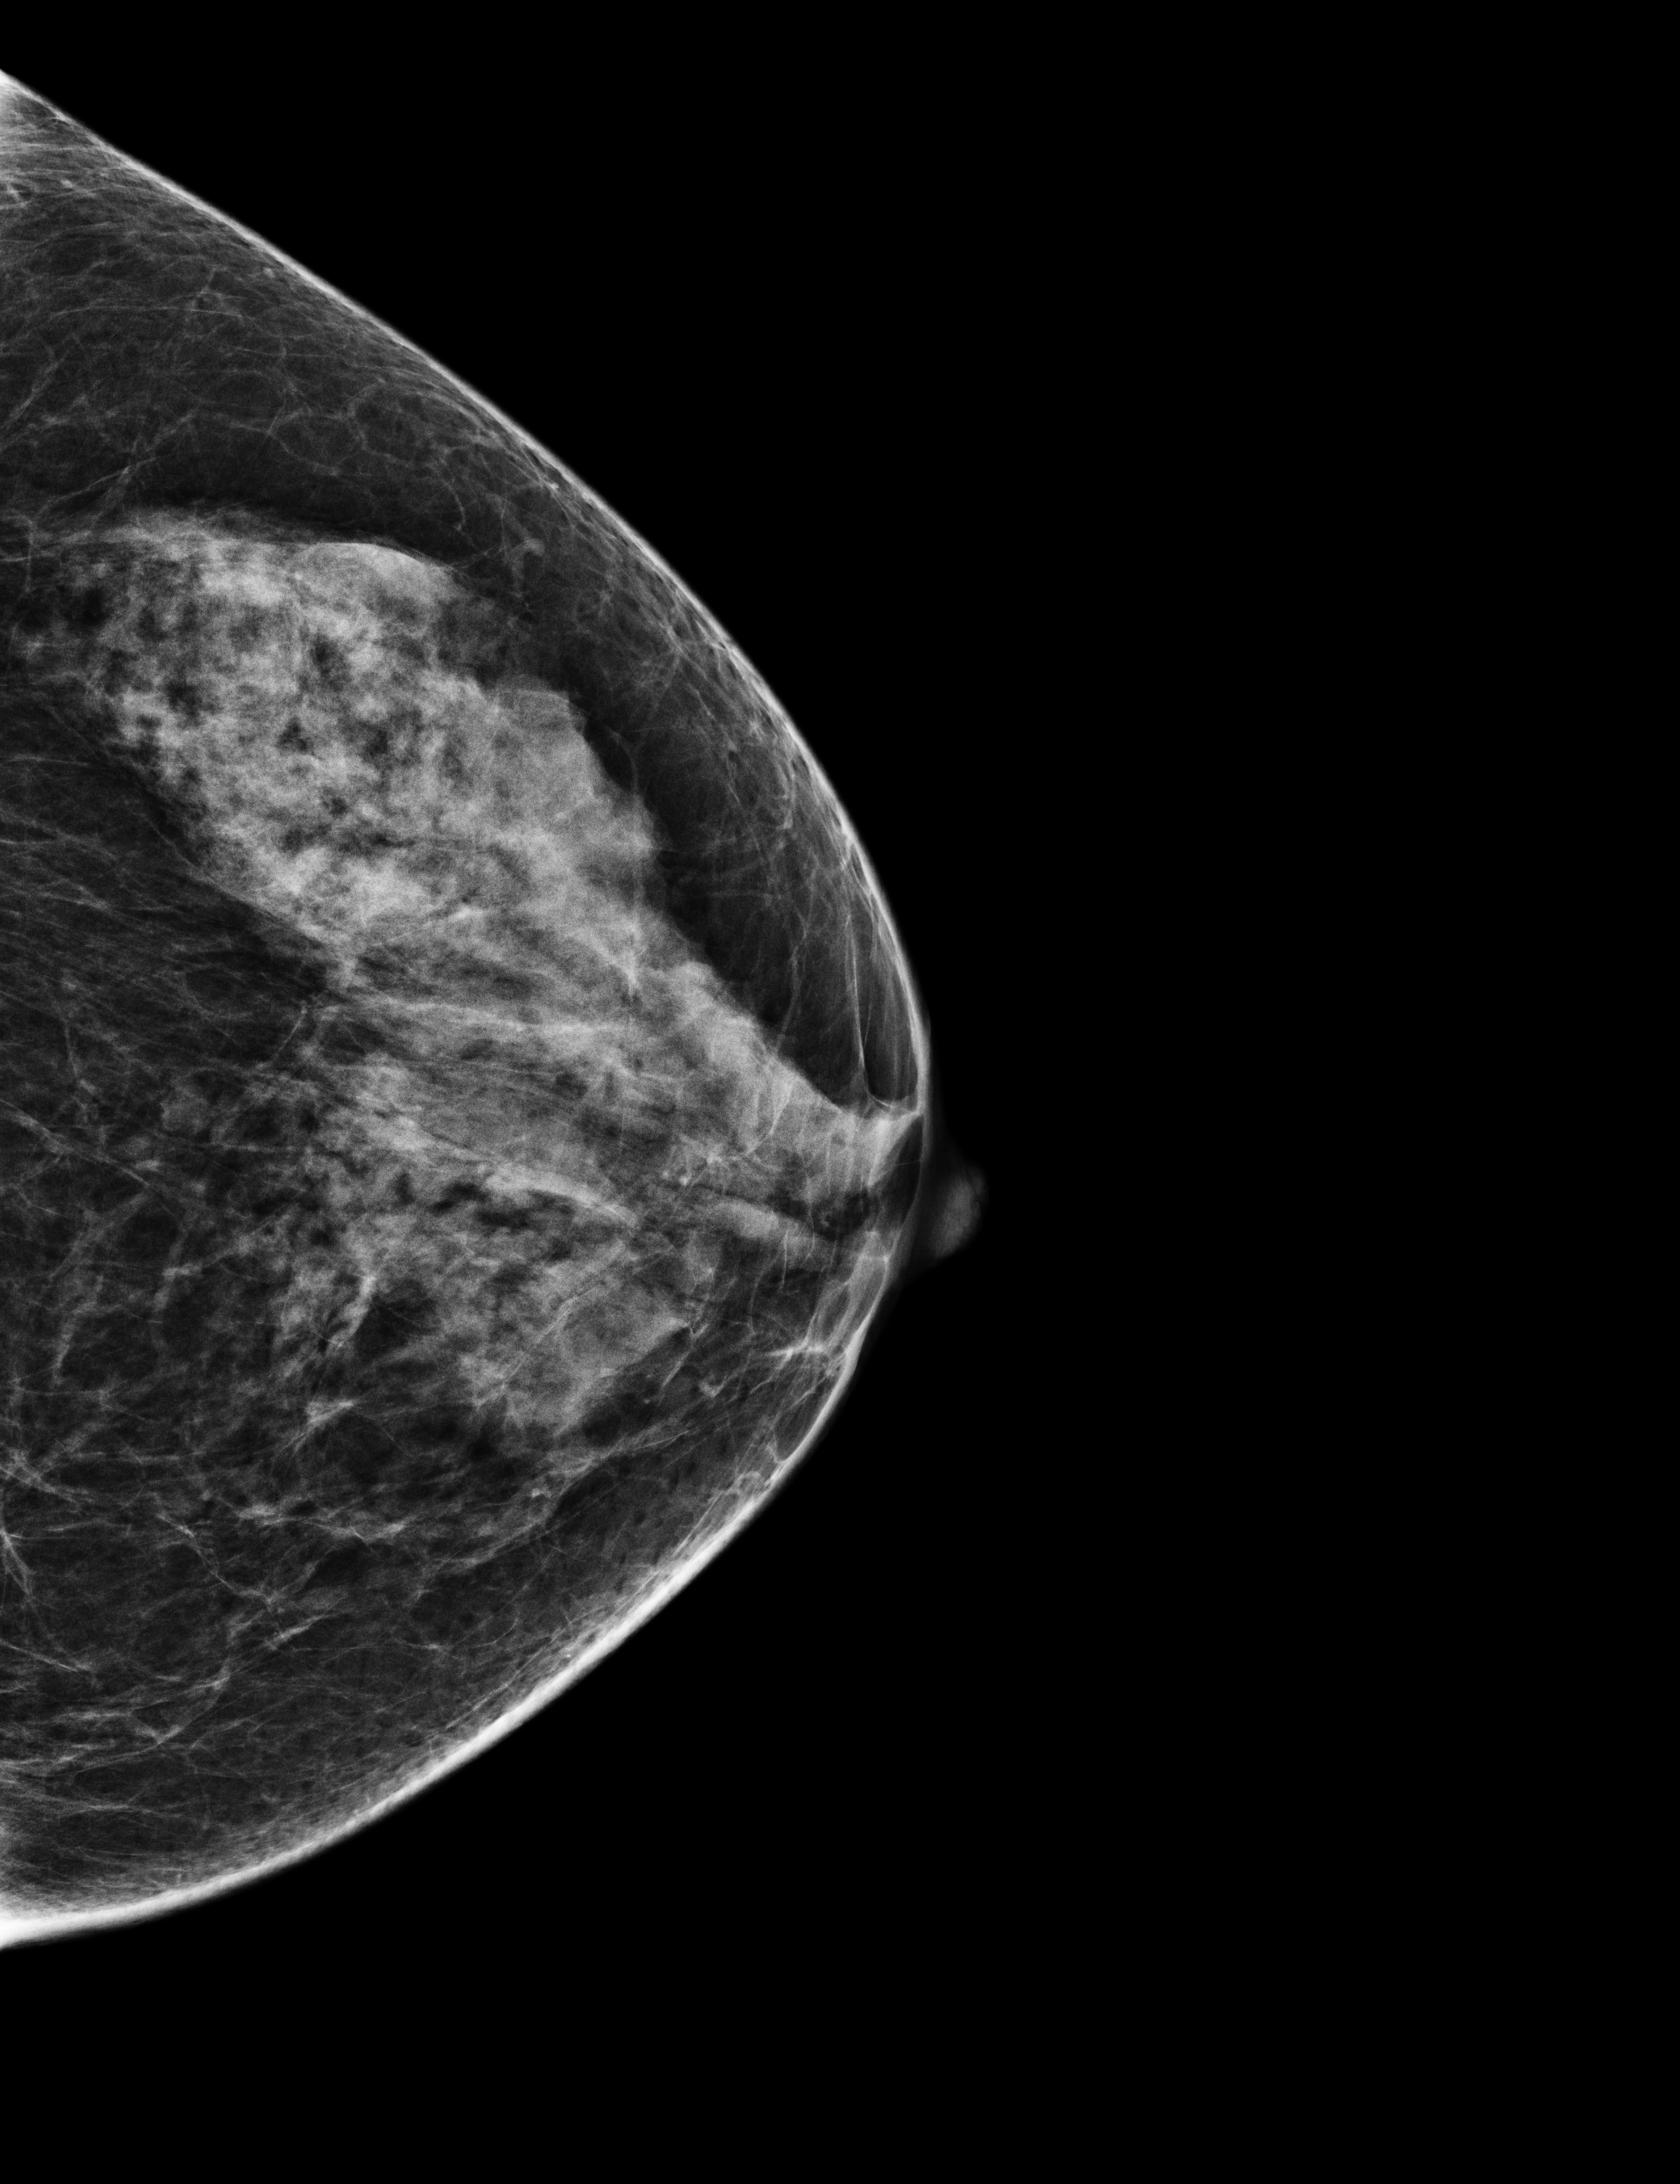
Annual screening mammography examination. Female patient, age 67 years.
Image type: full-field digital mammogram. Breast: left. Projection: CC view.